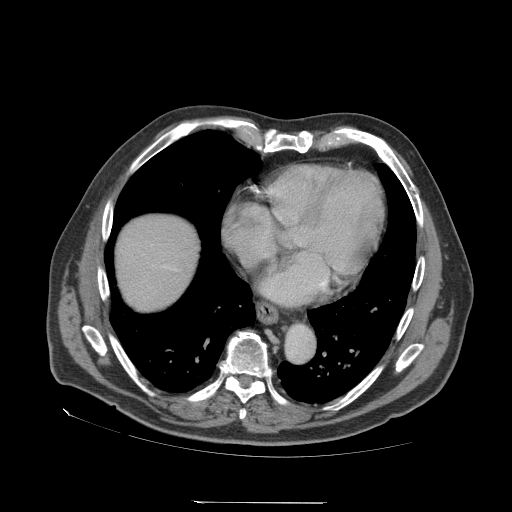
Contrast-enhanced abdominal CT (liver protocol), one axial slice. Position 71 of 83 along the scan axis. Reconstruction kernel STANDARD. Soft-tissue window (W 400 / L 40 HU). 2.5 mm slice thickness. 512 × 512 image matrix. From the clinical record (not read from this slice): diagnosis: hepatocellular carcinoma (patient treated with transarterial chemoembolisation; whether this scan precedes or follows treatment is not stated here); TNM stage (as recorded): Stage-I; Child-Pugh class: A; tumour differentiation: well differentiated.
Annotated regions visible in this slice (semi-automatic segmentation, software-assisted and operator-edited):
- liver parenchyma outside the tumour (the mass and vessels are separate outlines, so this box may not span the whole liver): bounding box (x1, y1, x2, y2) in pixels: (116, 214, 198, 310)